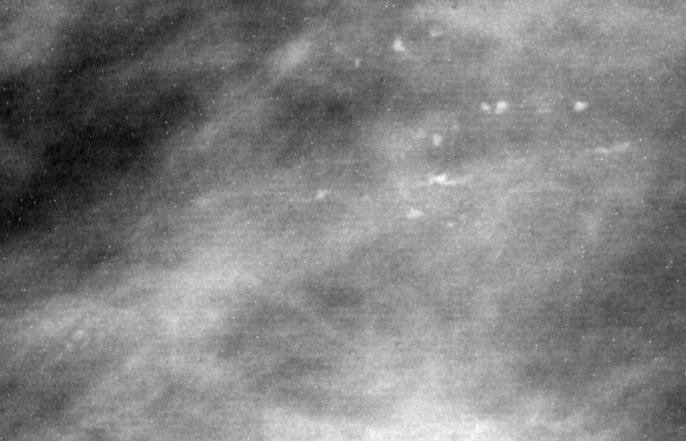
Cropped region of a digitized screen-film mammogram centred on a radiologist-marked abnormality; left breast; MLO view.
Marked abnormality: calcifications, morphology pleomorphic, distribution linear; BI-RADS assessment category 4; subtlety rating 3 on a 1 (subtle) to 5 (obvious) scale; pathology result (as recorded, not read from the image): malignant.